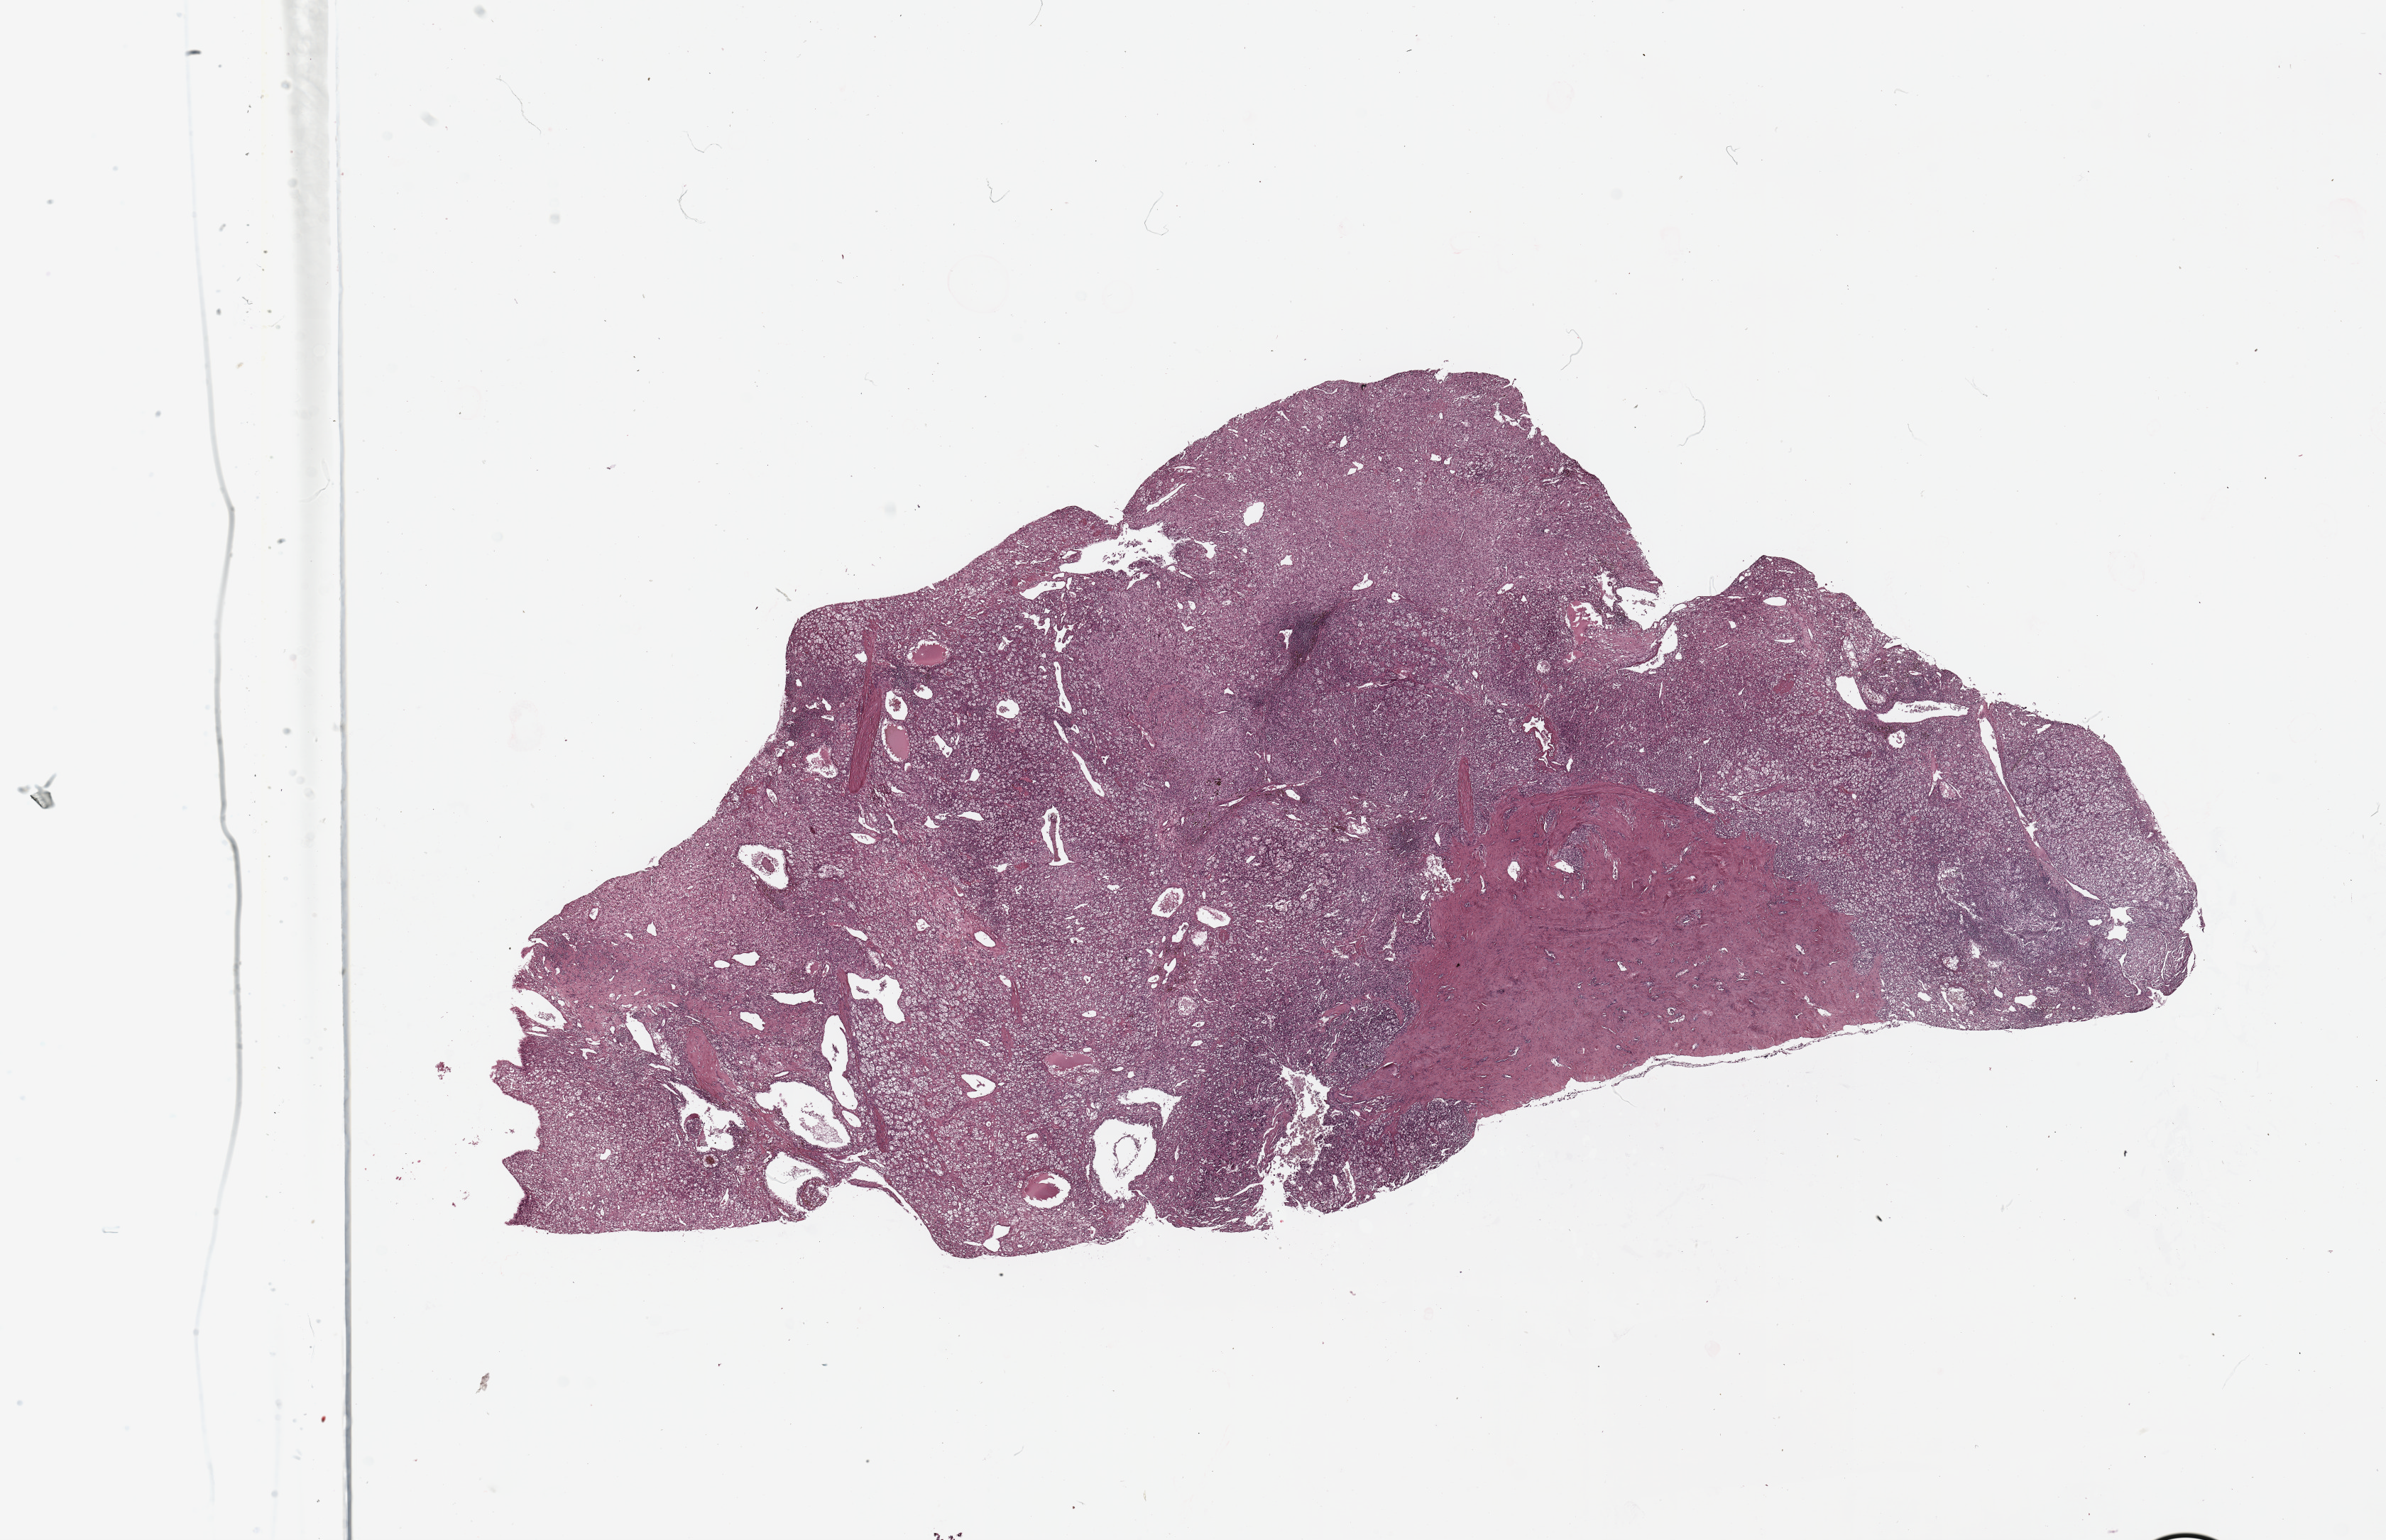
Hematoxylin and eosin (H&E) stained whole-slide image, a low-resolution overview of the entire scanned area, about 26.6 x 17.2 mm. Tumour tissue sample, sampled site: kidney. 51-year-old male patient. Histologic grade: G4 (undifferentiated). Slide review estimates, as recorded: tumour nuclei 85%, necrosis 5%.
* histologic diagnosis: Renal cell carcinoma, NOS
* AJCC pathologic stage: IV
* primary tumour site (as recorded): middle